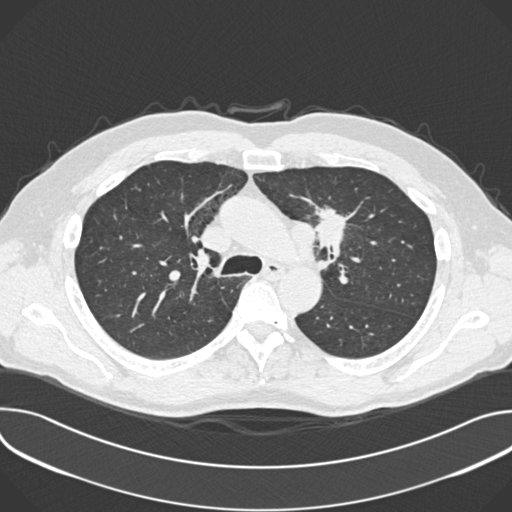
Low-dose screening chest CT, one axial slice. Slice 256 of 361 in the series (ordered by position). Reconstruction kernel B30f. 120 kVp. Lung window (W 1500 / L -600 HU). 1 mm slice thickness. 512 × 512 image matrix, field of view 380 × 380 mm.
Outlined on this slice (manually delineated by an expert):
- lesion 1 (tumor, upper lobe of left lung): bounding box [x1, y1, x2, y2] px = [316, 207, 348, 248]